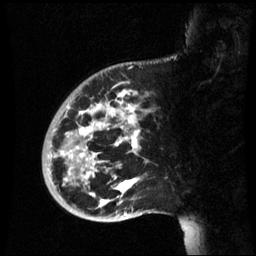
Breast MRI (dynamic contrast-enhanced), one sagittal slice. Dynamic contrast-enhanced series, image 2 of 3 at this slice position (ordered by acquisition). 1.5 T. TE 4.2 ms, TR 8.9 ms. 256 × 256 image matrix. Patient: female, 35 years. Case-level facts recorded for this patient, not image findings: setting: breast cancer imaged before/during neoadjuvant chemotherapy; receptor status: HR-positive, HER2-negative.
Outlined on this slice (semi-automatically segmented with operator editing):
- analysis volume of interest (the breast-tissue region the enhancement analysis was run in; not a lesion): bounding box (x1, y1, x2, y2) in pixels: (42, 74, 163, 221)
- tumour enhancement mask (voxels above the 70 % enhancement threshold inside the analysis volume of interest): (61, 92, 140, 207)